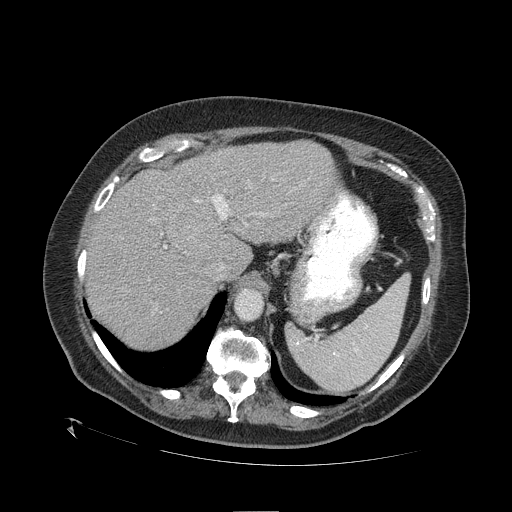
Contrast-enhanced abdominal CT (liver protocol), one axial slice. Reconstruction kernel STANDARD. 120 kVp. One of 2 acquisitions stored at this slice position. Soft-tissue window (W 400 / L 40 HU). 2.5 mm slice thickness. 512 × 512 image matrix, field of view 460 × 460 mm. Case-level facts recorded for this patient, not image findings: diagnosis: hepatocellular carcinoma (patient treated with transarterial chemoembolisation; whether this scan precedes or follows treatment is not stated here); TNM stage (as recorded): Stage-I; Child-Pugh class: A; tumour differentiation: no biopsy; tumour nodularity: uninodular.
Annotated regions visible in this slice (semi-automatic segmentation, software-assisted and operator-edited):
- liver parenchyma outside the tumour (the mass and vessels are separate outlines, so this box may not span the whole liver): box from (x=86, y=140) to (x=334, y=348) px
- mass: (x=165, y=201)–(x=218, y=255)
- liver vessels: (x=164, y=194)–(x=264, y=248)